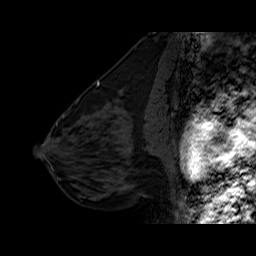
Breast MRI (dynamic contrast-enhanced), one sagittal slice; slice 28 of 60 in the series (ordered by position); dynamic contrast-enhanced series, time point 2 of 6 at this slice position (early post-contrast); 1.5 T; TE 6.3 ms, TR 32.5 ms; 256 × 256 image matrix. Female patient. From the clinical record (not read from this slice): setting: breast cancer imaged before/during neoadjuvant chemotherapy; receptor status: triple-negative.
Annotated regions visible in this slice (semi-automatic segmentation, software-assisted and operator-edited):
- analysis volume of interest (the breast-tissue region the enhancement analysis was run in; not a lesion): bounding box [x1, y1, x2, y2] px = [102, 127, 162, 186]
- tumour enhancement mask (voxels above the 100 % enhancement threshold inside the analysis volume of interest): [128, 148, 131, 151]